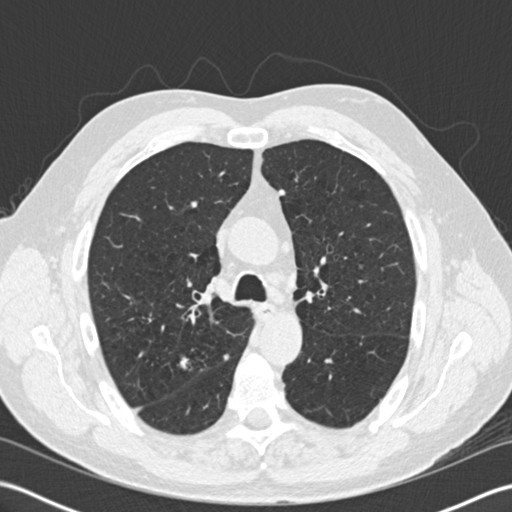
Low-dose screening chest CT, axial slice; second screening round (one year after baseline); lung window (W 1500 / L -600 HU); 2 mm slice thickness; 120 kVp; 512 × 512 image matrix. Male, age 65 years at enrolment. Former smoker at enrolment.
Expert-annotated lung lesion, bounding box <159,345,204,384> (left, top, right, bottom; pixels). The screening reader recorded 6 non-calcified nodules or masses ≥4 mm on this exam (right upper lobe, left upper lobe, left upper lobe, right upper lobe, left upper lobe, right upper lobe); which of them this box marks is not recorded. Lung cancer was diagnosed 421 days after this screen (after the third annual screen): adenocarcinoma, NOS, right upper lobe, moderately differentiated (G2), stage IA (AJCC 6th edition), 16 mm at pathology.